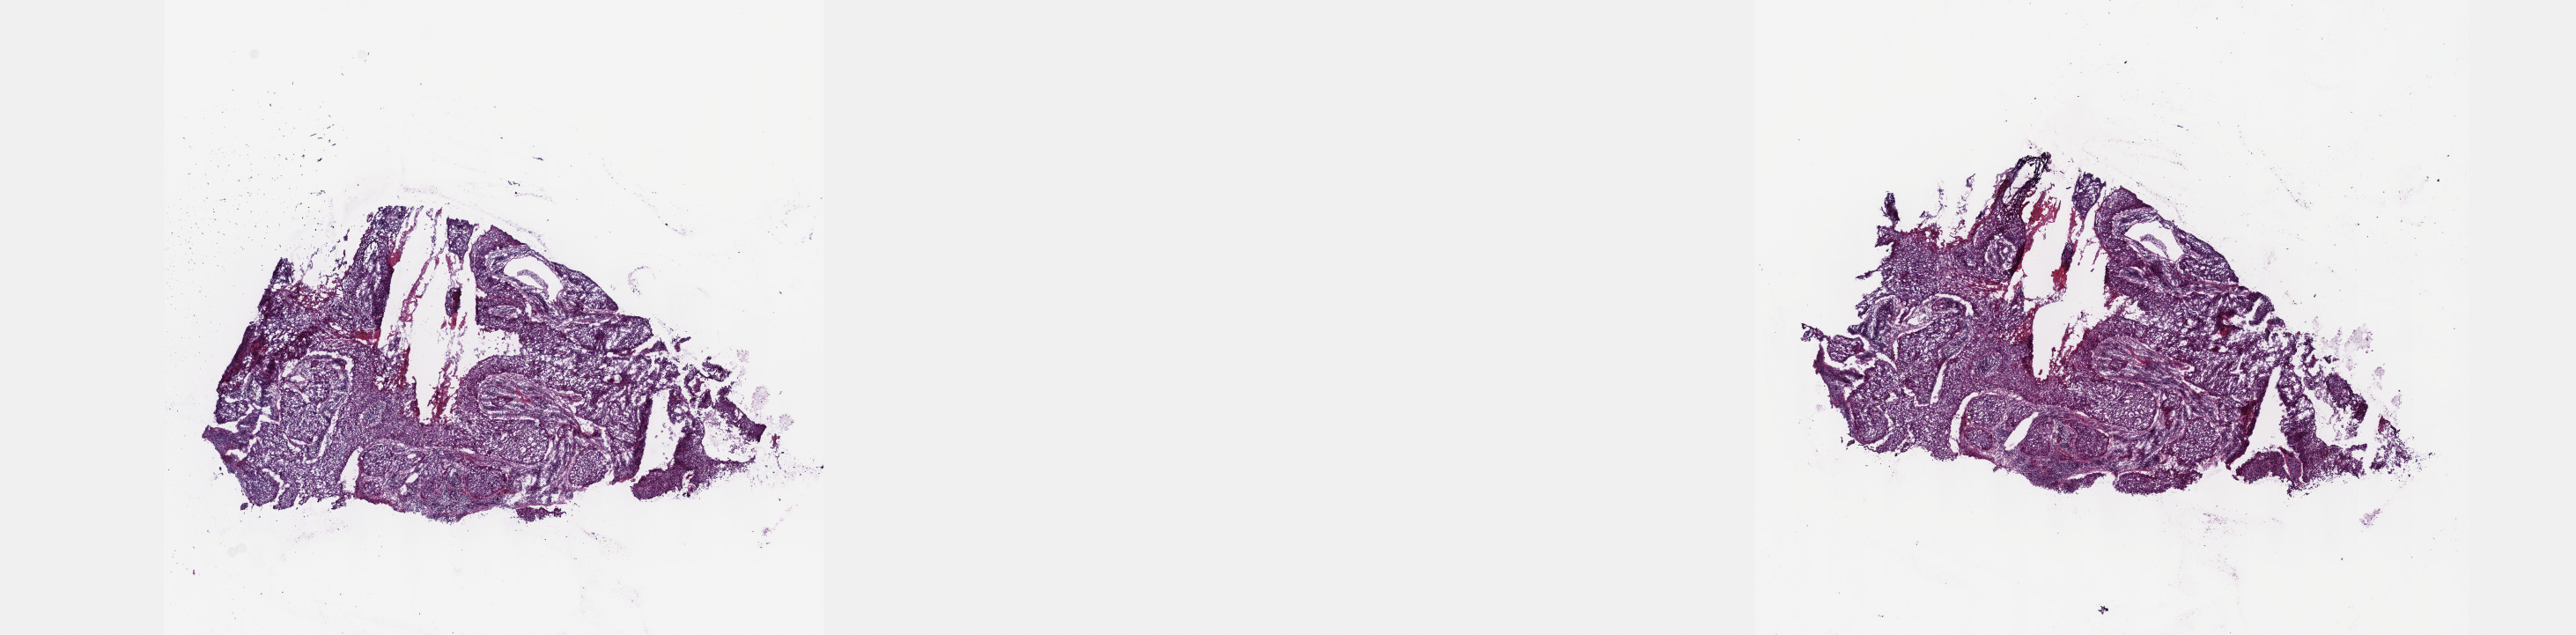
Hematoxylin and eosin (H&E) stained whole-slide image — whole scanned area (about 23.6 x 5.8 mm, from a 40x scan) shown as a low-resolution overview, frozen section from the top of the tissue portion, sample: primary tumour, cervix. Female patient; age at initial diagnosis 42 years. Histologic grade: G2 (moderately differentiated). Pathologist review of this section (percent, as recorded): tumour cells 80%, tumour nuclei 80%, normal cells 10%, stromal cells 10%, necrosis 0%. Inflammatory infiltration, as recorded: lymphocyte infiltration 5%, monocyte infiltration 0%, neutrophil infiltration 2%.
* FIGO stage: IIB
* pathologic diagnosis: Squamous cell carcinoma, NOS